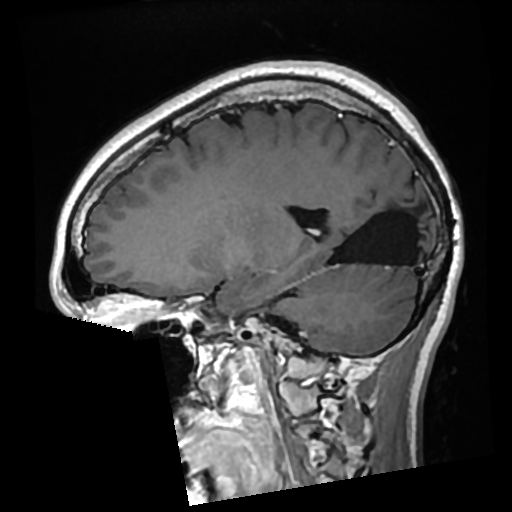
Brain MRI from a brain-tumour surgery series, one sagittal slice. Slice 111 of 276 in the series (ordered by position). T1-weighted post-contrast. 0.7 mm slice thickness. 512 × 512 image matrix. From the clinical record (not read from this slice): histopathology: Glioma with ependymal features; WHO grade: 2.
Annotated regions visible in this slice (expert manual segmentation):
- previous resection cavity: bounding box (x1, y1, x2, y2) in pixels: (332, 192, 424, 266)